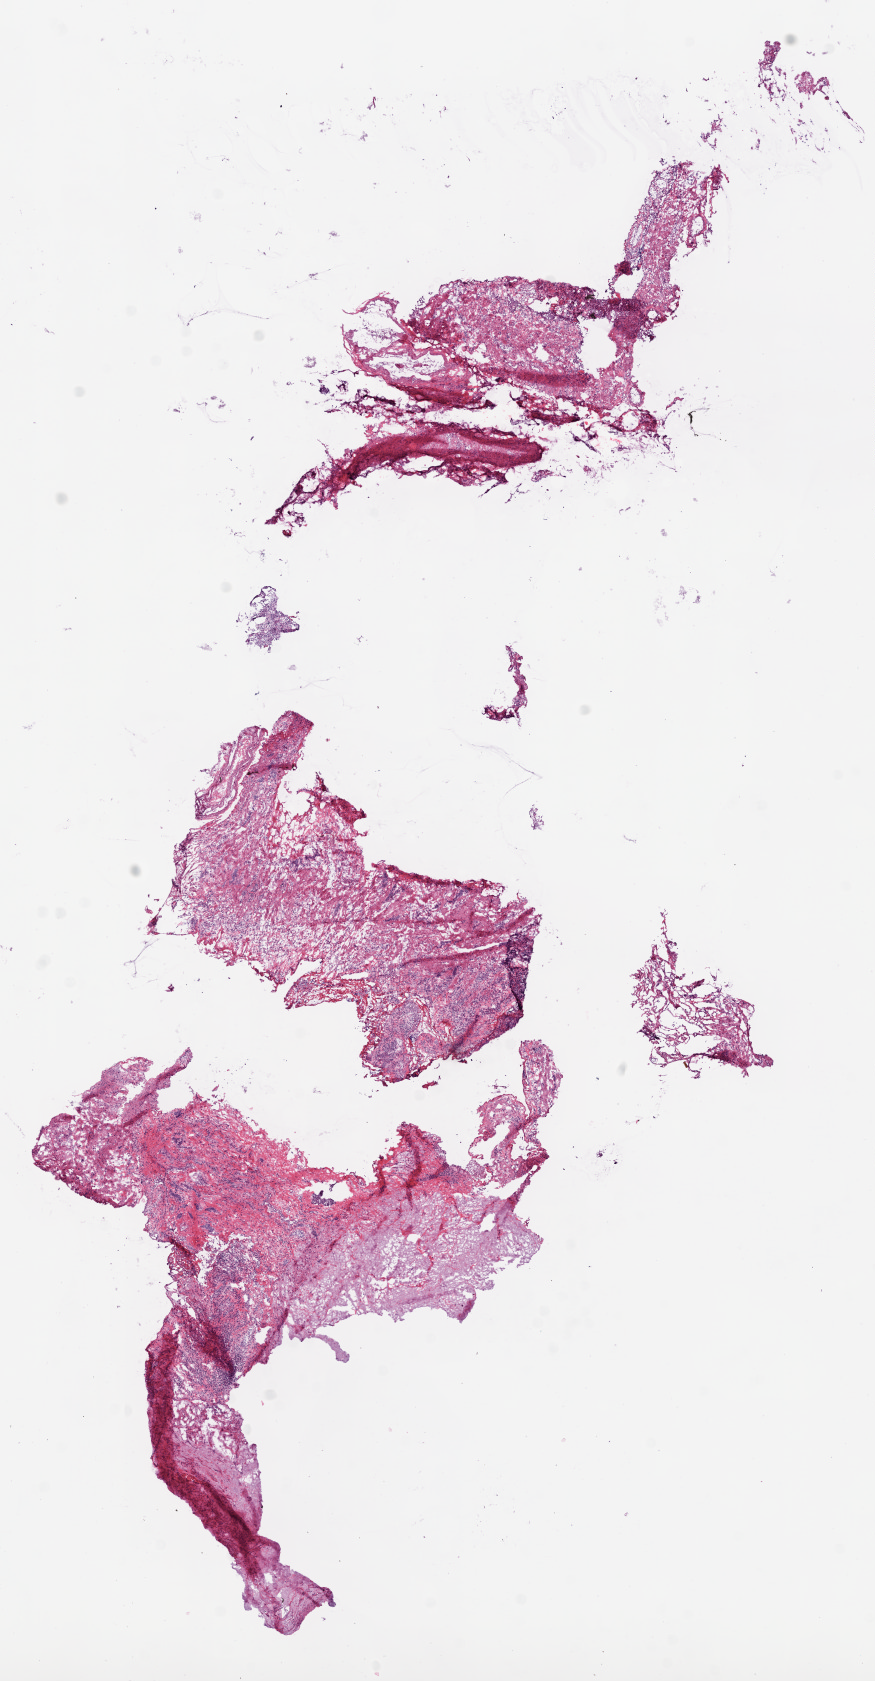
H&E whole-slide image, shown as a low-resolution overview of the whole scanned area (about 7.0 x 13.5 mm), frozen section, solid tissue normal (non-tumour tissue) sample from the ovary. Female patient; age at initial diagnosis 64 years.
• this section: solid tissue normal (non-tumour) sample from the same patient
• patient diagnosis: Serous cystadenocarcinoma, NOS